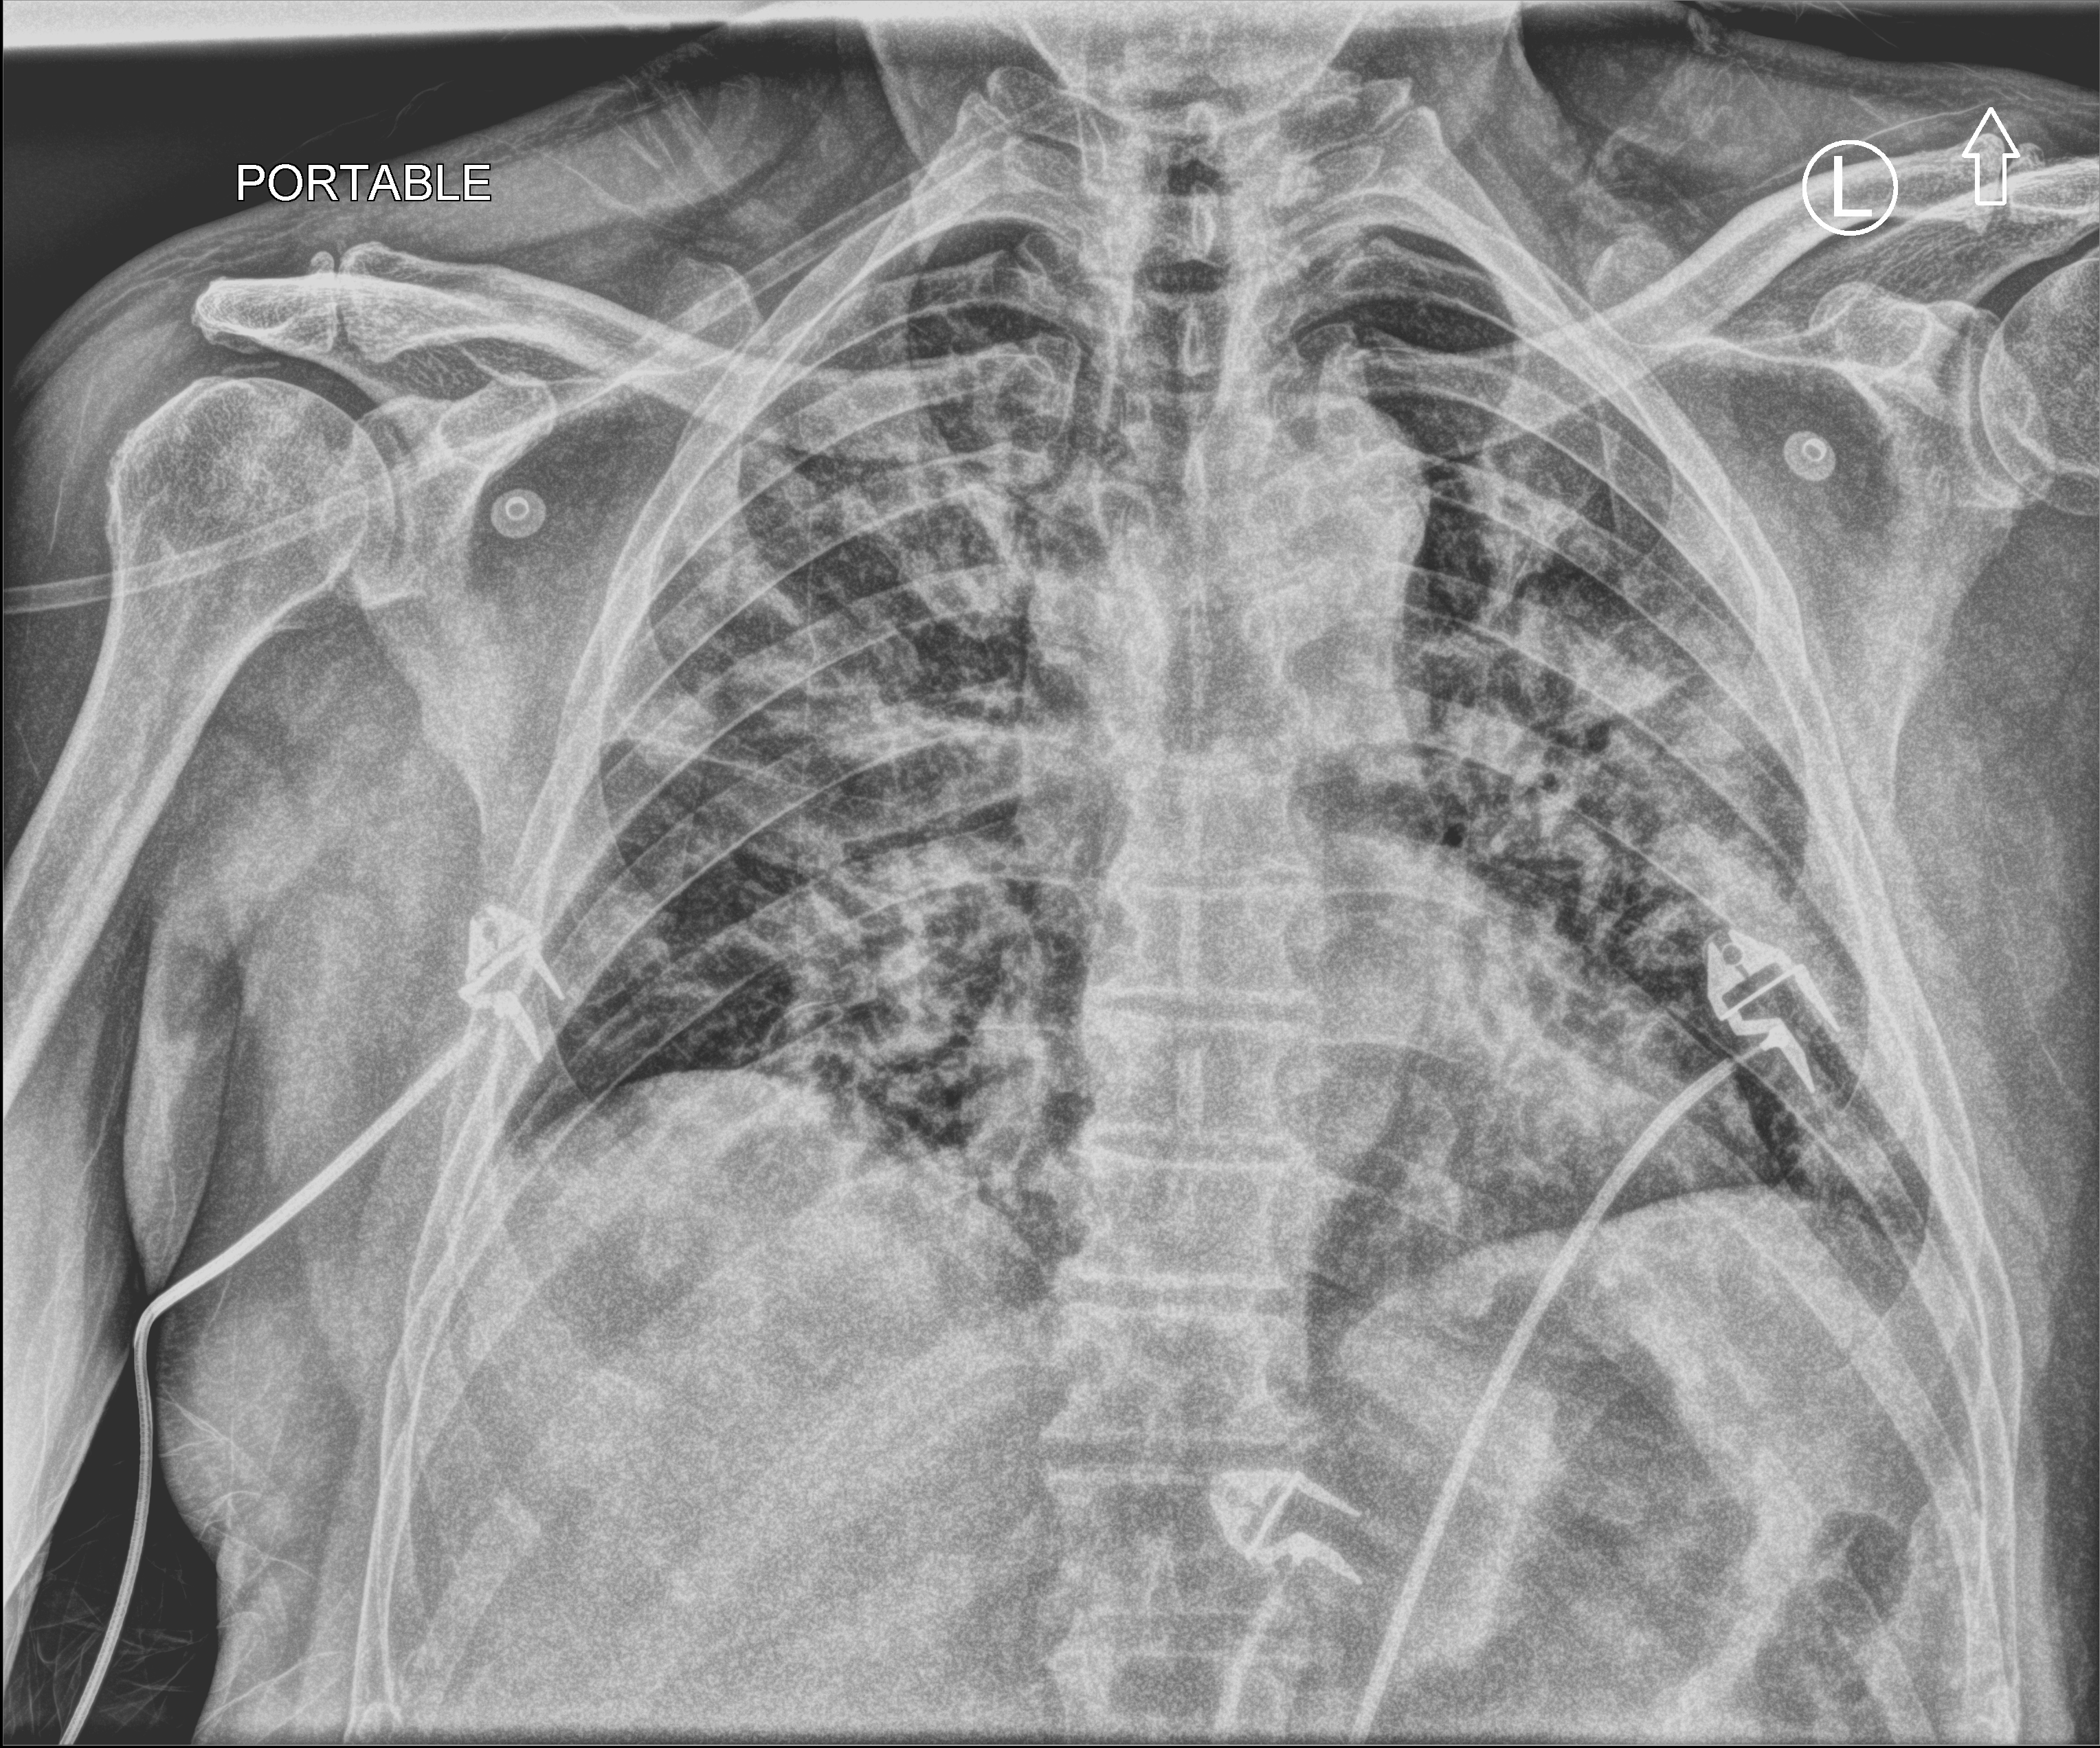
Chest X-ray (portable); anteroposterior (AP) projection. Male patient hospitalised with COVID-19, age 60–74 years.
Hospital-stay facts (about this admission, not read from this image; timing relative to this image not recorded): COPD (admission record): no; admitted to intensive care during this hospital stay: yes; length of hospital stay: 20 days.